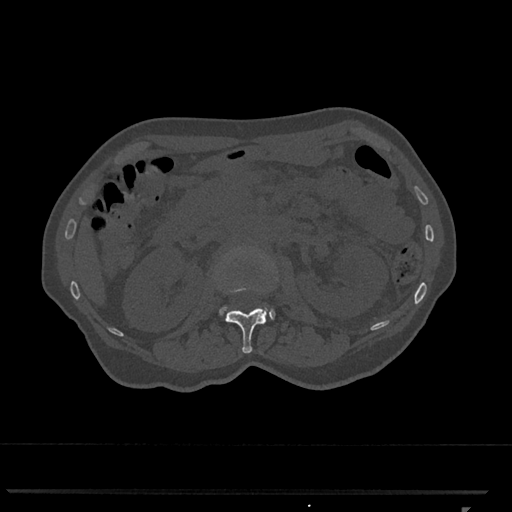
CT including the spine, one axial slice; position 381 of 793 along the scan axis; reconstruction kernel Br40s/3; bone window (W 1800 / L 400 HU); 512 × 512 image matrix, field of view 380 × 380 mm. Female patient, age 62 years. Case-level facts recorded for this patient, not image findings: primary cancer: renal.
Structures marked on this image (semi-automatically segmented with operator editing):
- L1 vertebra: bounding box [x1, y1, x2, y2] px = [225, 248, 267, 354]
- L2 vertebra: [219, 306, 275, 320]